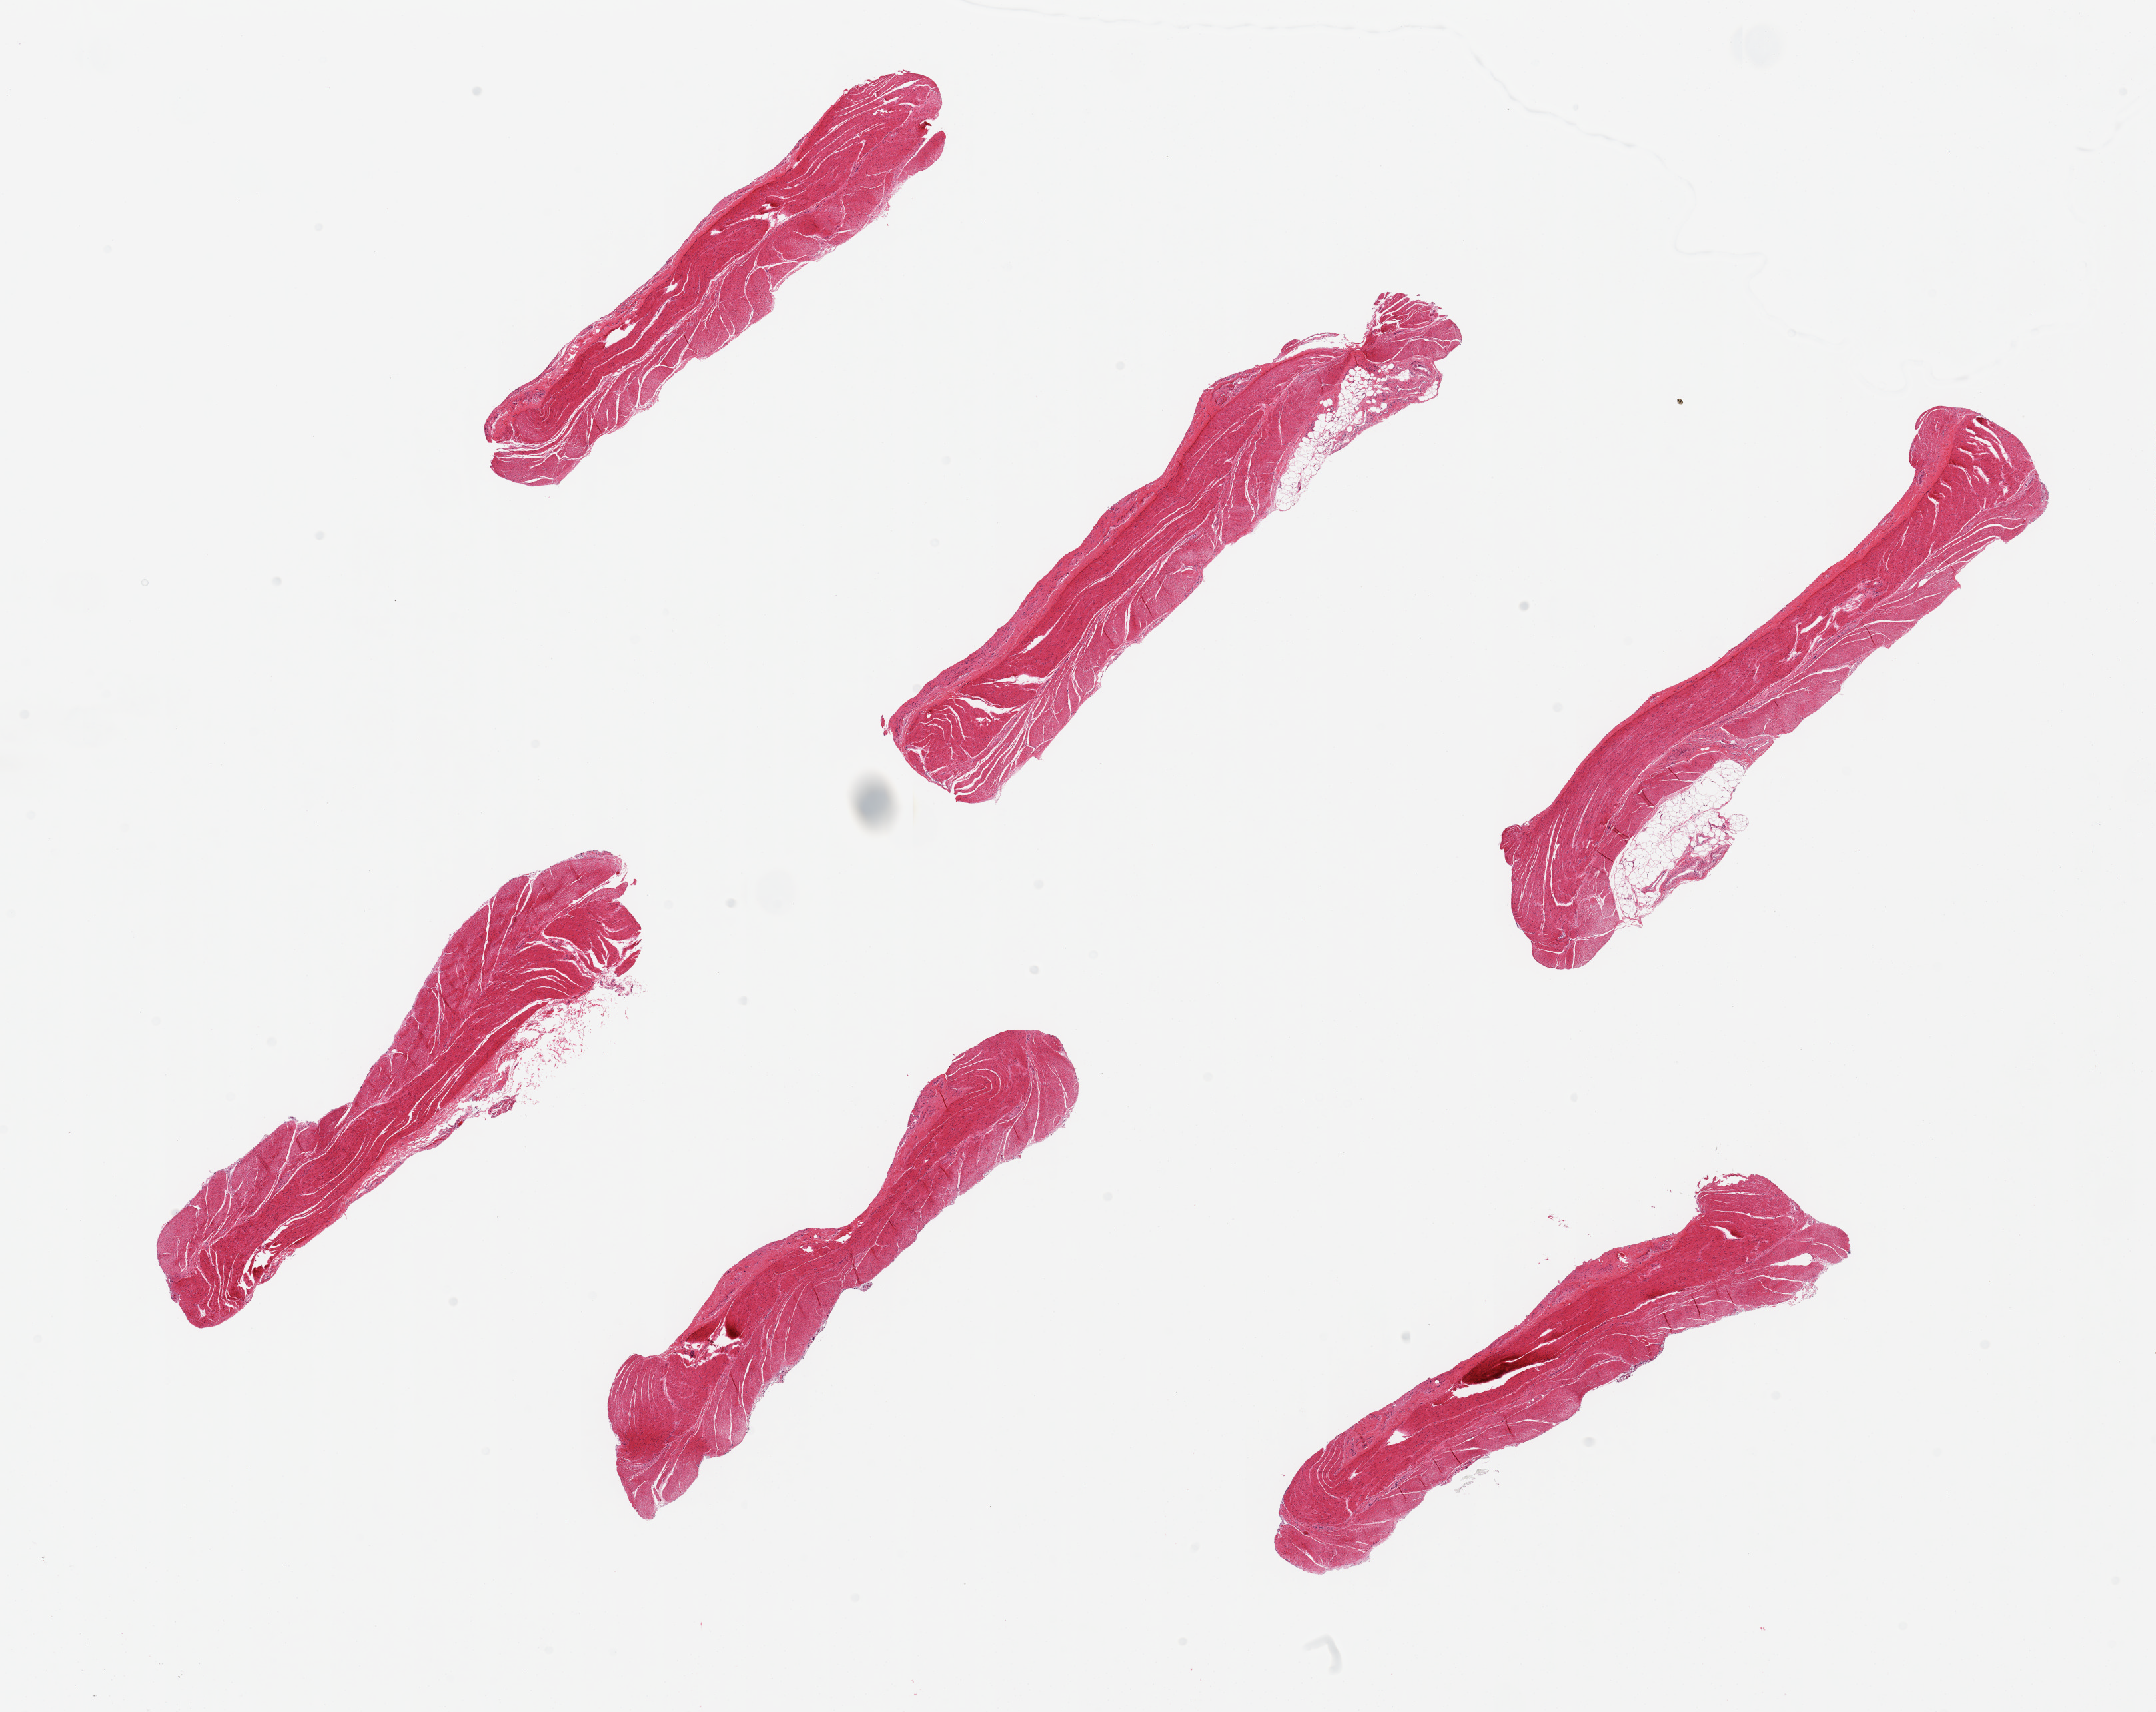
Haematoxylin and eosin whole-slide image, brightfield — whole scanned area (about 25.6 x 20.3 mm) shown as a low-resolution overview, PAXgene-fixed paraffin-embedded (PFPE) section, section of sigmoid colon (target tissue), donor tissue sample. Donor: female.
* reviewer comment on this tissue sample: 6 pieces; several foci of fat up to 20%